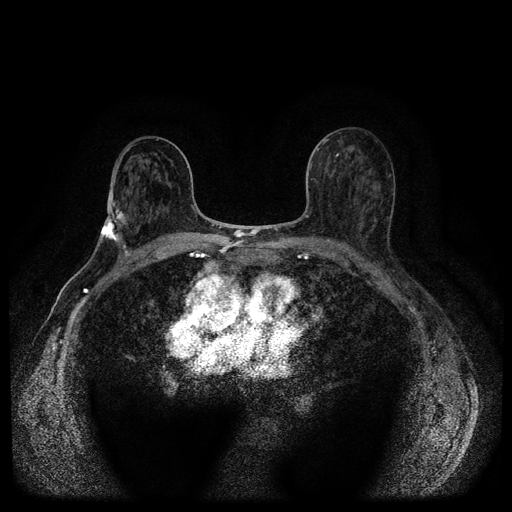
Breast MRI (dynamic contrast-enhanced, multi-phase), one axial slice; slice 60 of 116 in the series (ordered by position); dynamic contrast-enhanced series, time point 2 of 5 at this slice position (early post-contrast); 1.5 T; TE 2.7 ms, TR 5.4 ms; 2 mm slice thickness; 512 × 512 image matrix, field of view 340 × 340 mm. Patient: female, 75 years.
Outlined on this slice (semi-automatically segmented with operator editing):
- breast lesion (labelled 'tumour' in the annotation; benign lesions carry a separate 'benign' label): bounding box <100,200,128,243> (left, top, right, bottom; pixels)